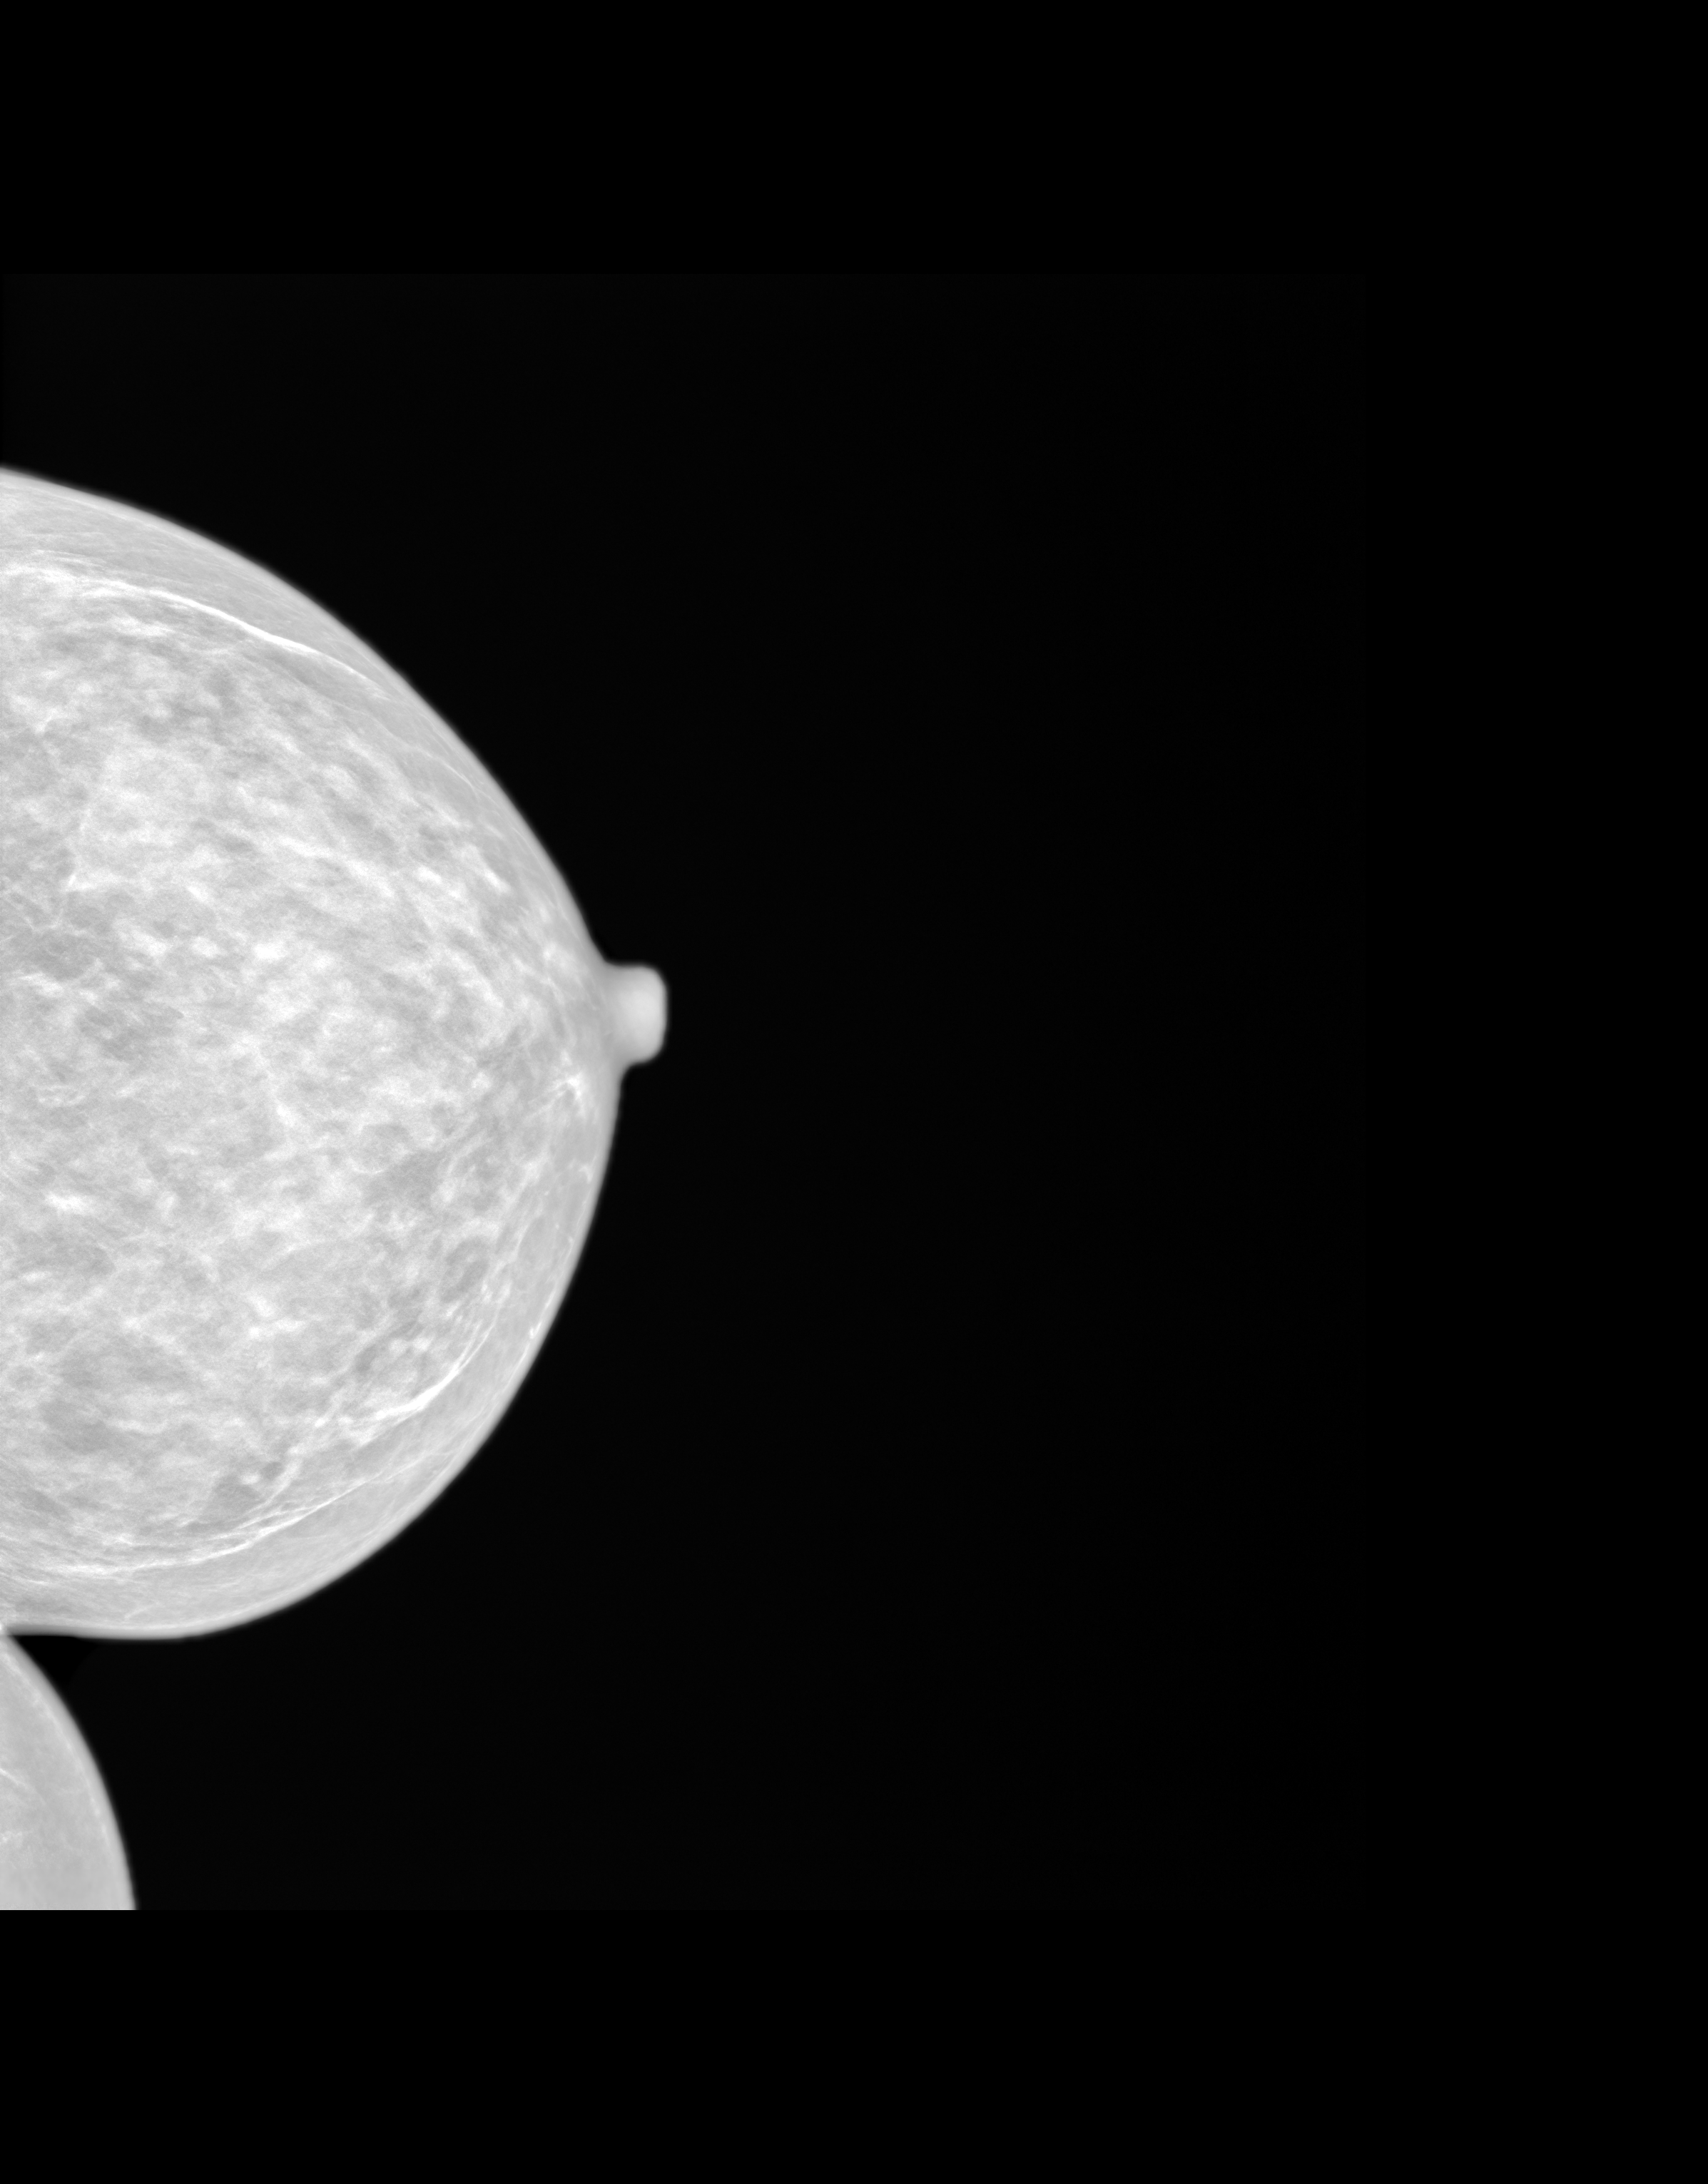
Synthesized 2-D mammogram reconstructed from digital breast tomosynthesis; left breast; CC view; screening examination. Patient aged 60 years (female).
Final BI-RADS assessment for this screening round (tomosynthesis exam, both breasts): category 1.